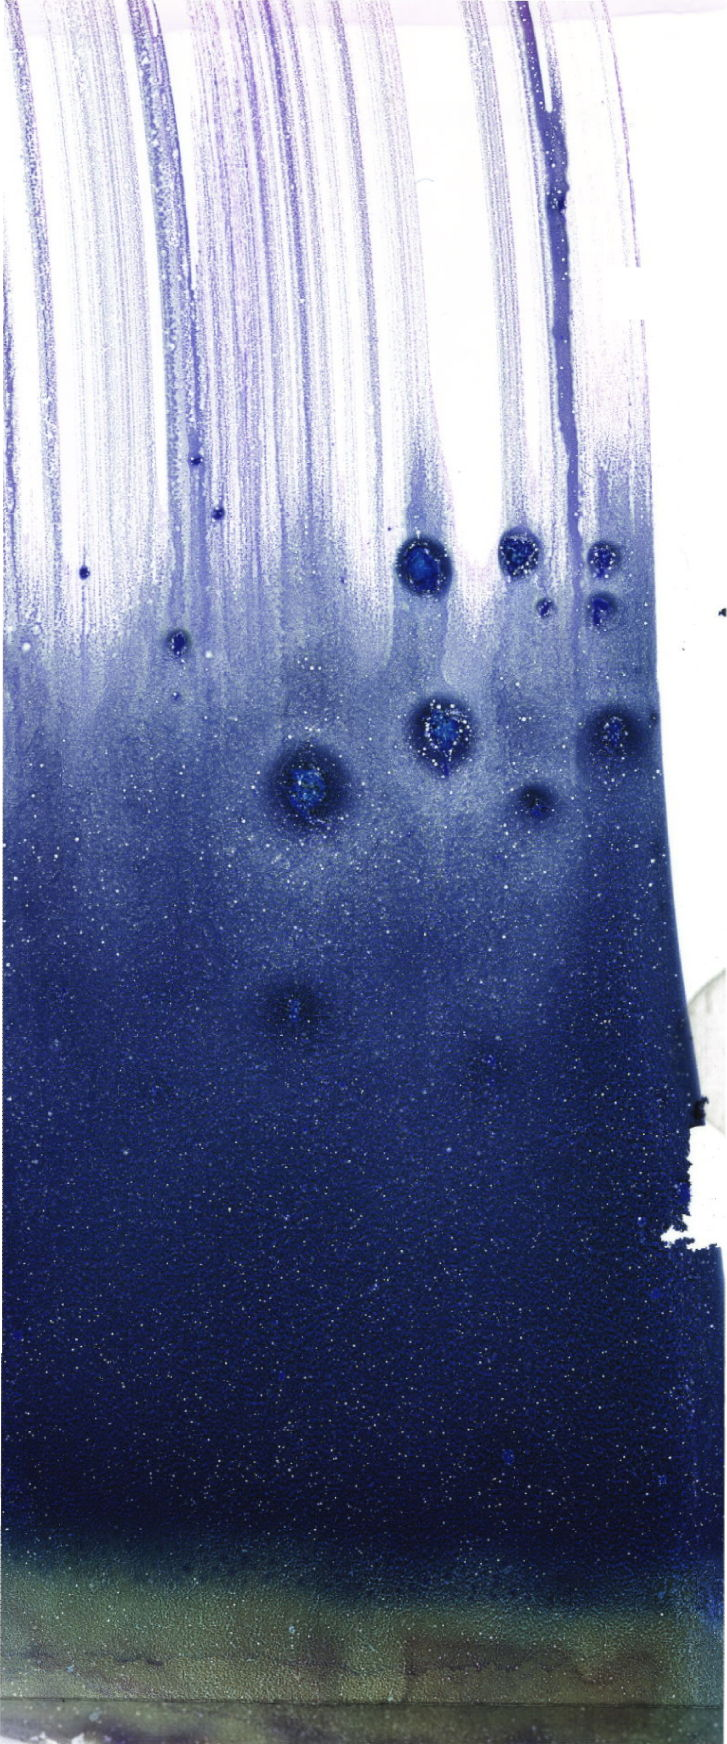
May-Grünwald-Giemsa (MGG)-stained marrow aspirate smear (whole slide) — whole scanned area (about 20.6 x 49.4 mm) shown as a low-resolution overview. Patient sex: female.
- diagnosis: B Acute Lymphoblastic Leukemia